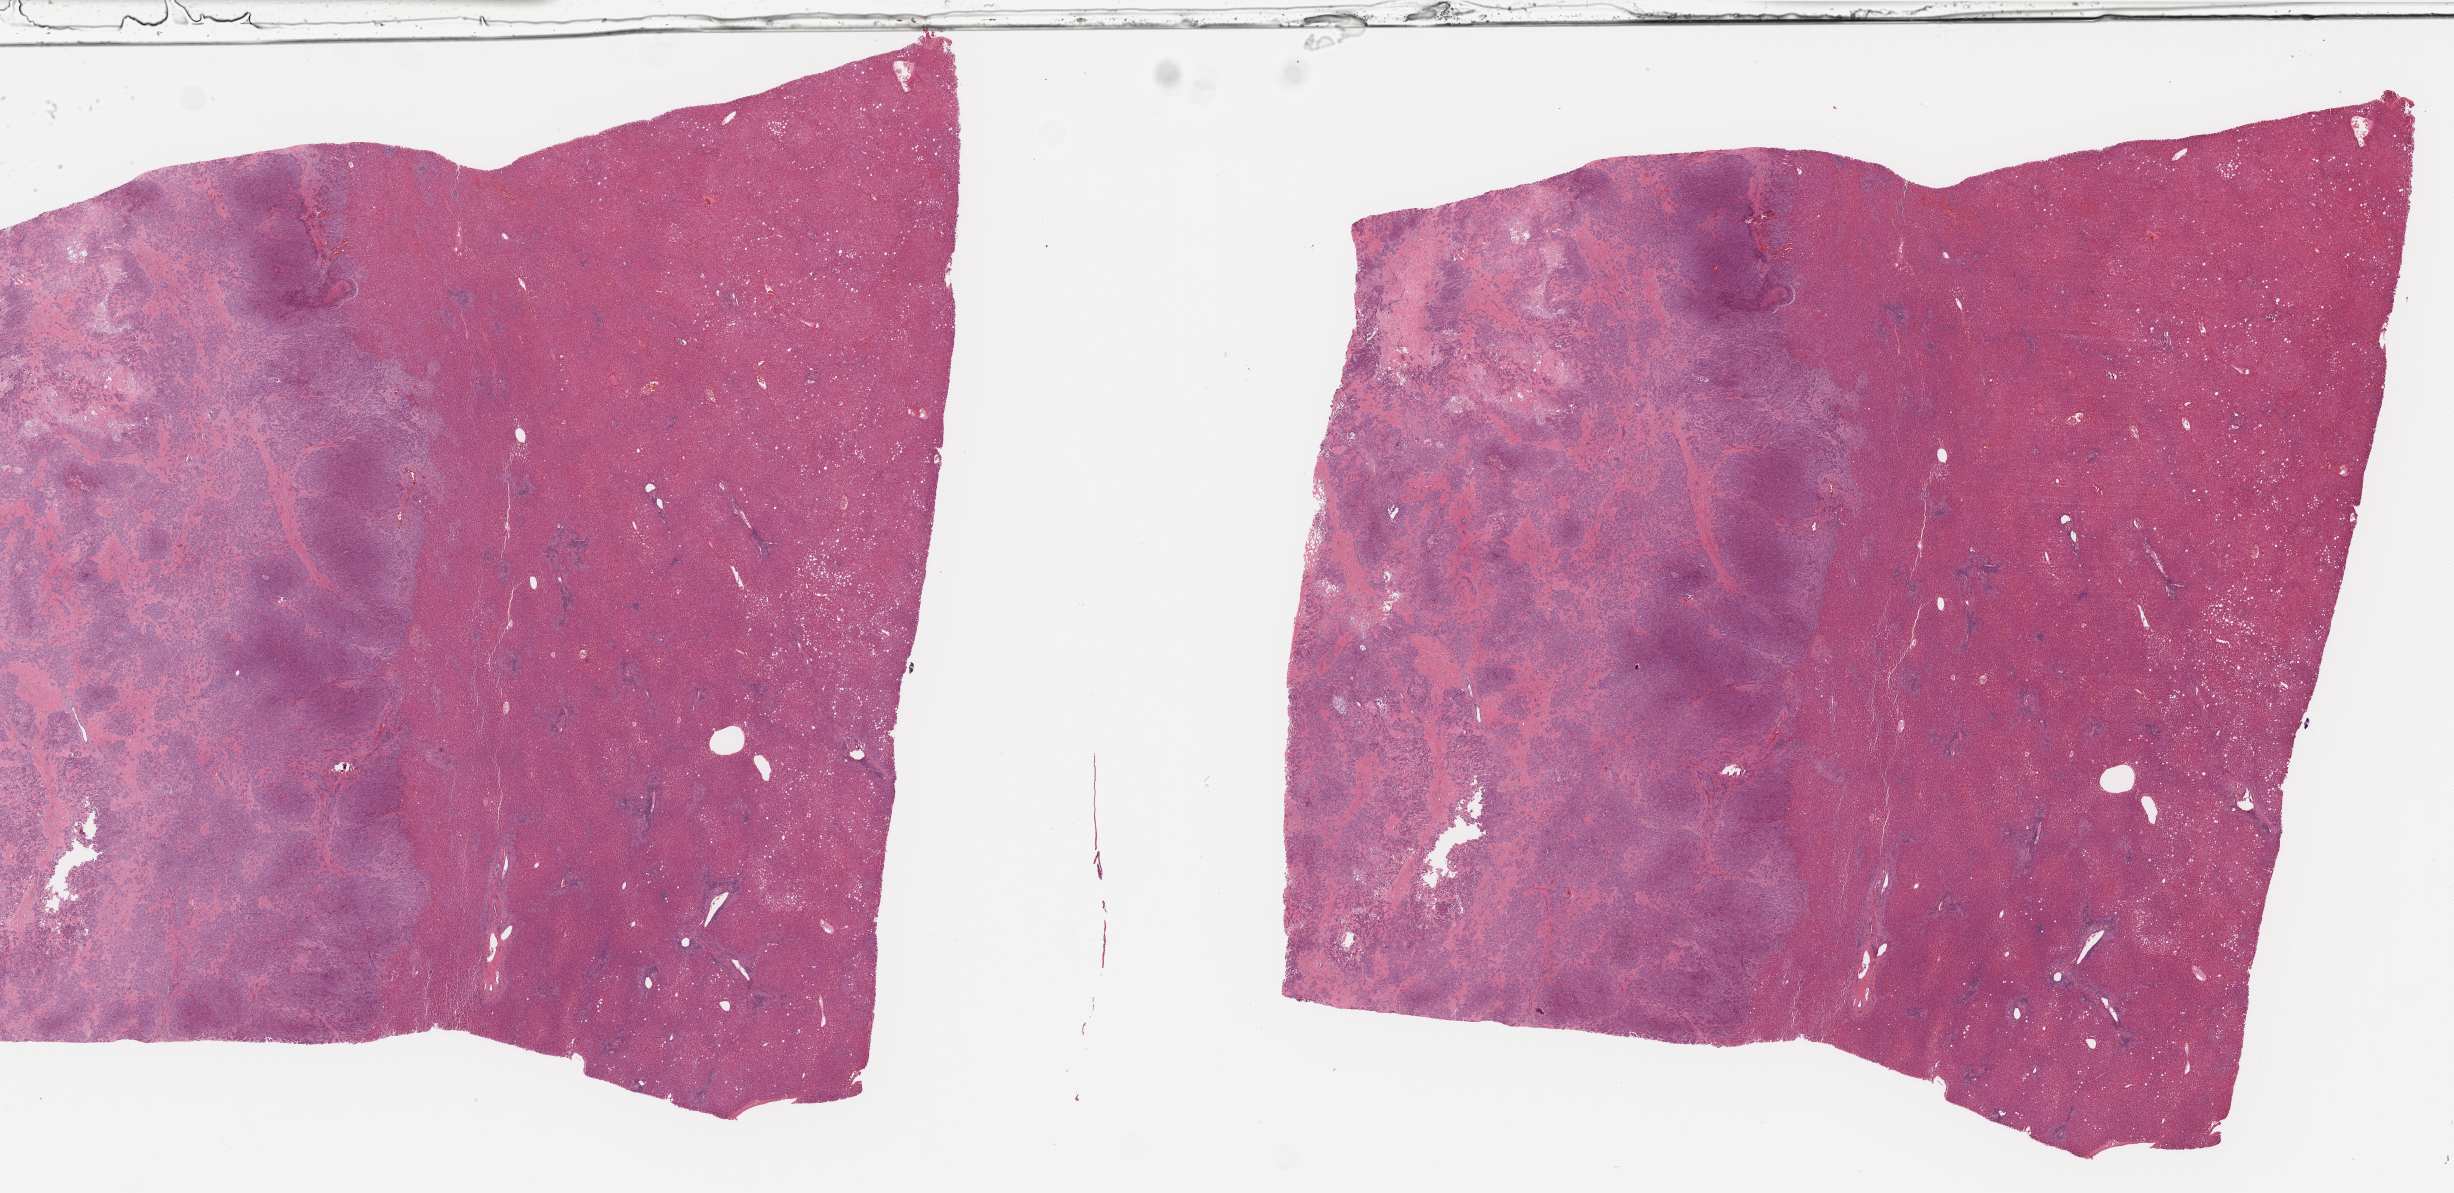
Whole-slide histology image, H&E-stained — whole scanned area (about 39.7 x 19.3 mm) shown as a low-resolution overview; formalin-fixed paraffin-embedded (FFPE) diagnostic section; sample: primary tumour, bile duct. Male, age 57 years at initial diagnosis. Histologic grade: G3 (poorly differentiated).
- diagnosis: Cholangiocarcinoma (intrahepatic bile duct)
- AJCC pathologic stage: I